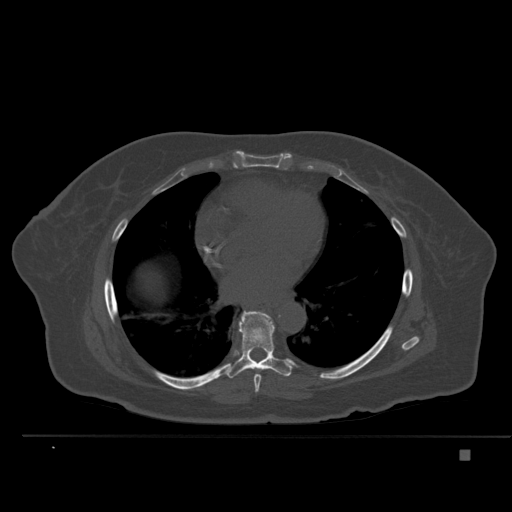
CT including the spine, one axial slice; bone window (W 1800 / L 400 HU); 512 × 512 image matrix, field of view 422 × 422 mm. Female patient, age 74 years. From the clinical record (not read from this slice): primary cancer: colon.
Structures marked on this image (semi-automatically segmented with operator editing):
- T7 vertebra: bounding box <254,375,262,393> (left, top, right, bottom; pixels)
- T8 vertebra: <225,311,292,379>